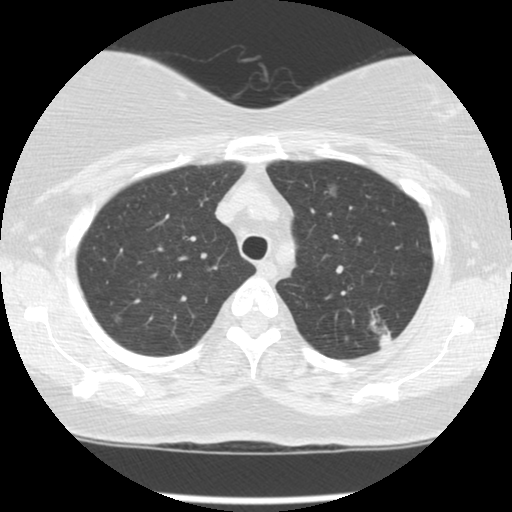
Chest CT (low-dose screening protocol), one axial image; third annual screen; lung window (W 1500 / L -600 HU); standard (soft-tissue) reconstruction kernel (STANDARD); slice 24 of 127 in the series; 512 × 512 image matrix. Female, age 56 years at enrolment. Current smoker at enrolment.
- Expert reader's lesion annotation, bounding box <339,304,414,363> (left, top, right, bottom; pixels).
- The screening reader recorded 4 non-calcified nodules or masses ≥4 mm on this exam (left upper lobe, left upper lobe, left upper lobe, right upper lobe); which of them this box marks is not recorded.
- Official screen result: positive, other.
- Lung cancer was diagnosed 49 days after this screen: adenocarcinoma, NOS, left upper lobe, moderately differentiated (G2), stage IA (AJCC 6th edition), 10 mm at pathology.